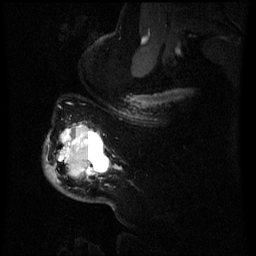
Breast MRI (dynamic contrast-enhanced), one sagittal slice. Dynamic contrast-enhanced series, image 2 of 3 at this slice position (ordered by acquisition). 1.5 T. TE 4.2 ms, TR 8 ms. 256 × 256 image matrix, field of view 200 × 200 mm. Patient: female, 50 years.
Outlined on this slice (semi-automatic segmentation, software-assisted and operator-edited):
- analysis volume of interest (the breast-tissue region the enhancement analysis was run in; not a lesion): box from (x=47, y=124) to (x=110, y=181) px
- tumour enhancement mask (voxels above the 70 % enhancement threshold inside the analysis volume of interest): (x=65, y=136)–(x=94, y=175)